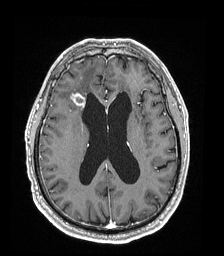
Brain MRI from a brain-tumour surgery series, one axial slice; slice 80 of 192 in the series (ordered by position); T1-weighted post-contrast; 224 × 256 image matrix, field of view 224 × 256 mm. Case-level facts recorded for this patient, not image findings: histopathology: Astrocytoma; WHO grade: 4; IDH mutation: yes; tumour location: Right Frontal.
Outlined on this slice (outlined manually by an expert reader):
- tumour: bounding box [x1, y1, x2, y2] px = [70, 93, 86, 108]